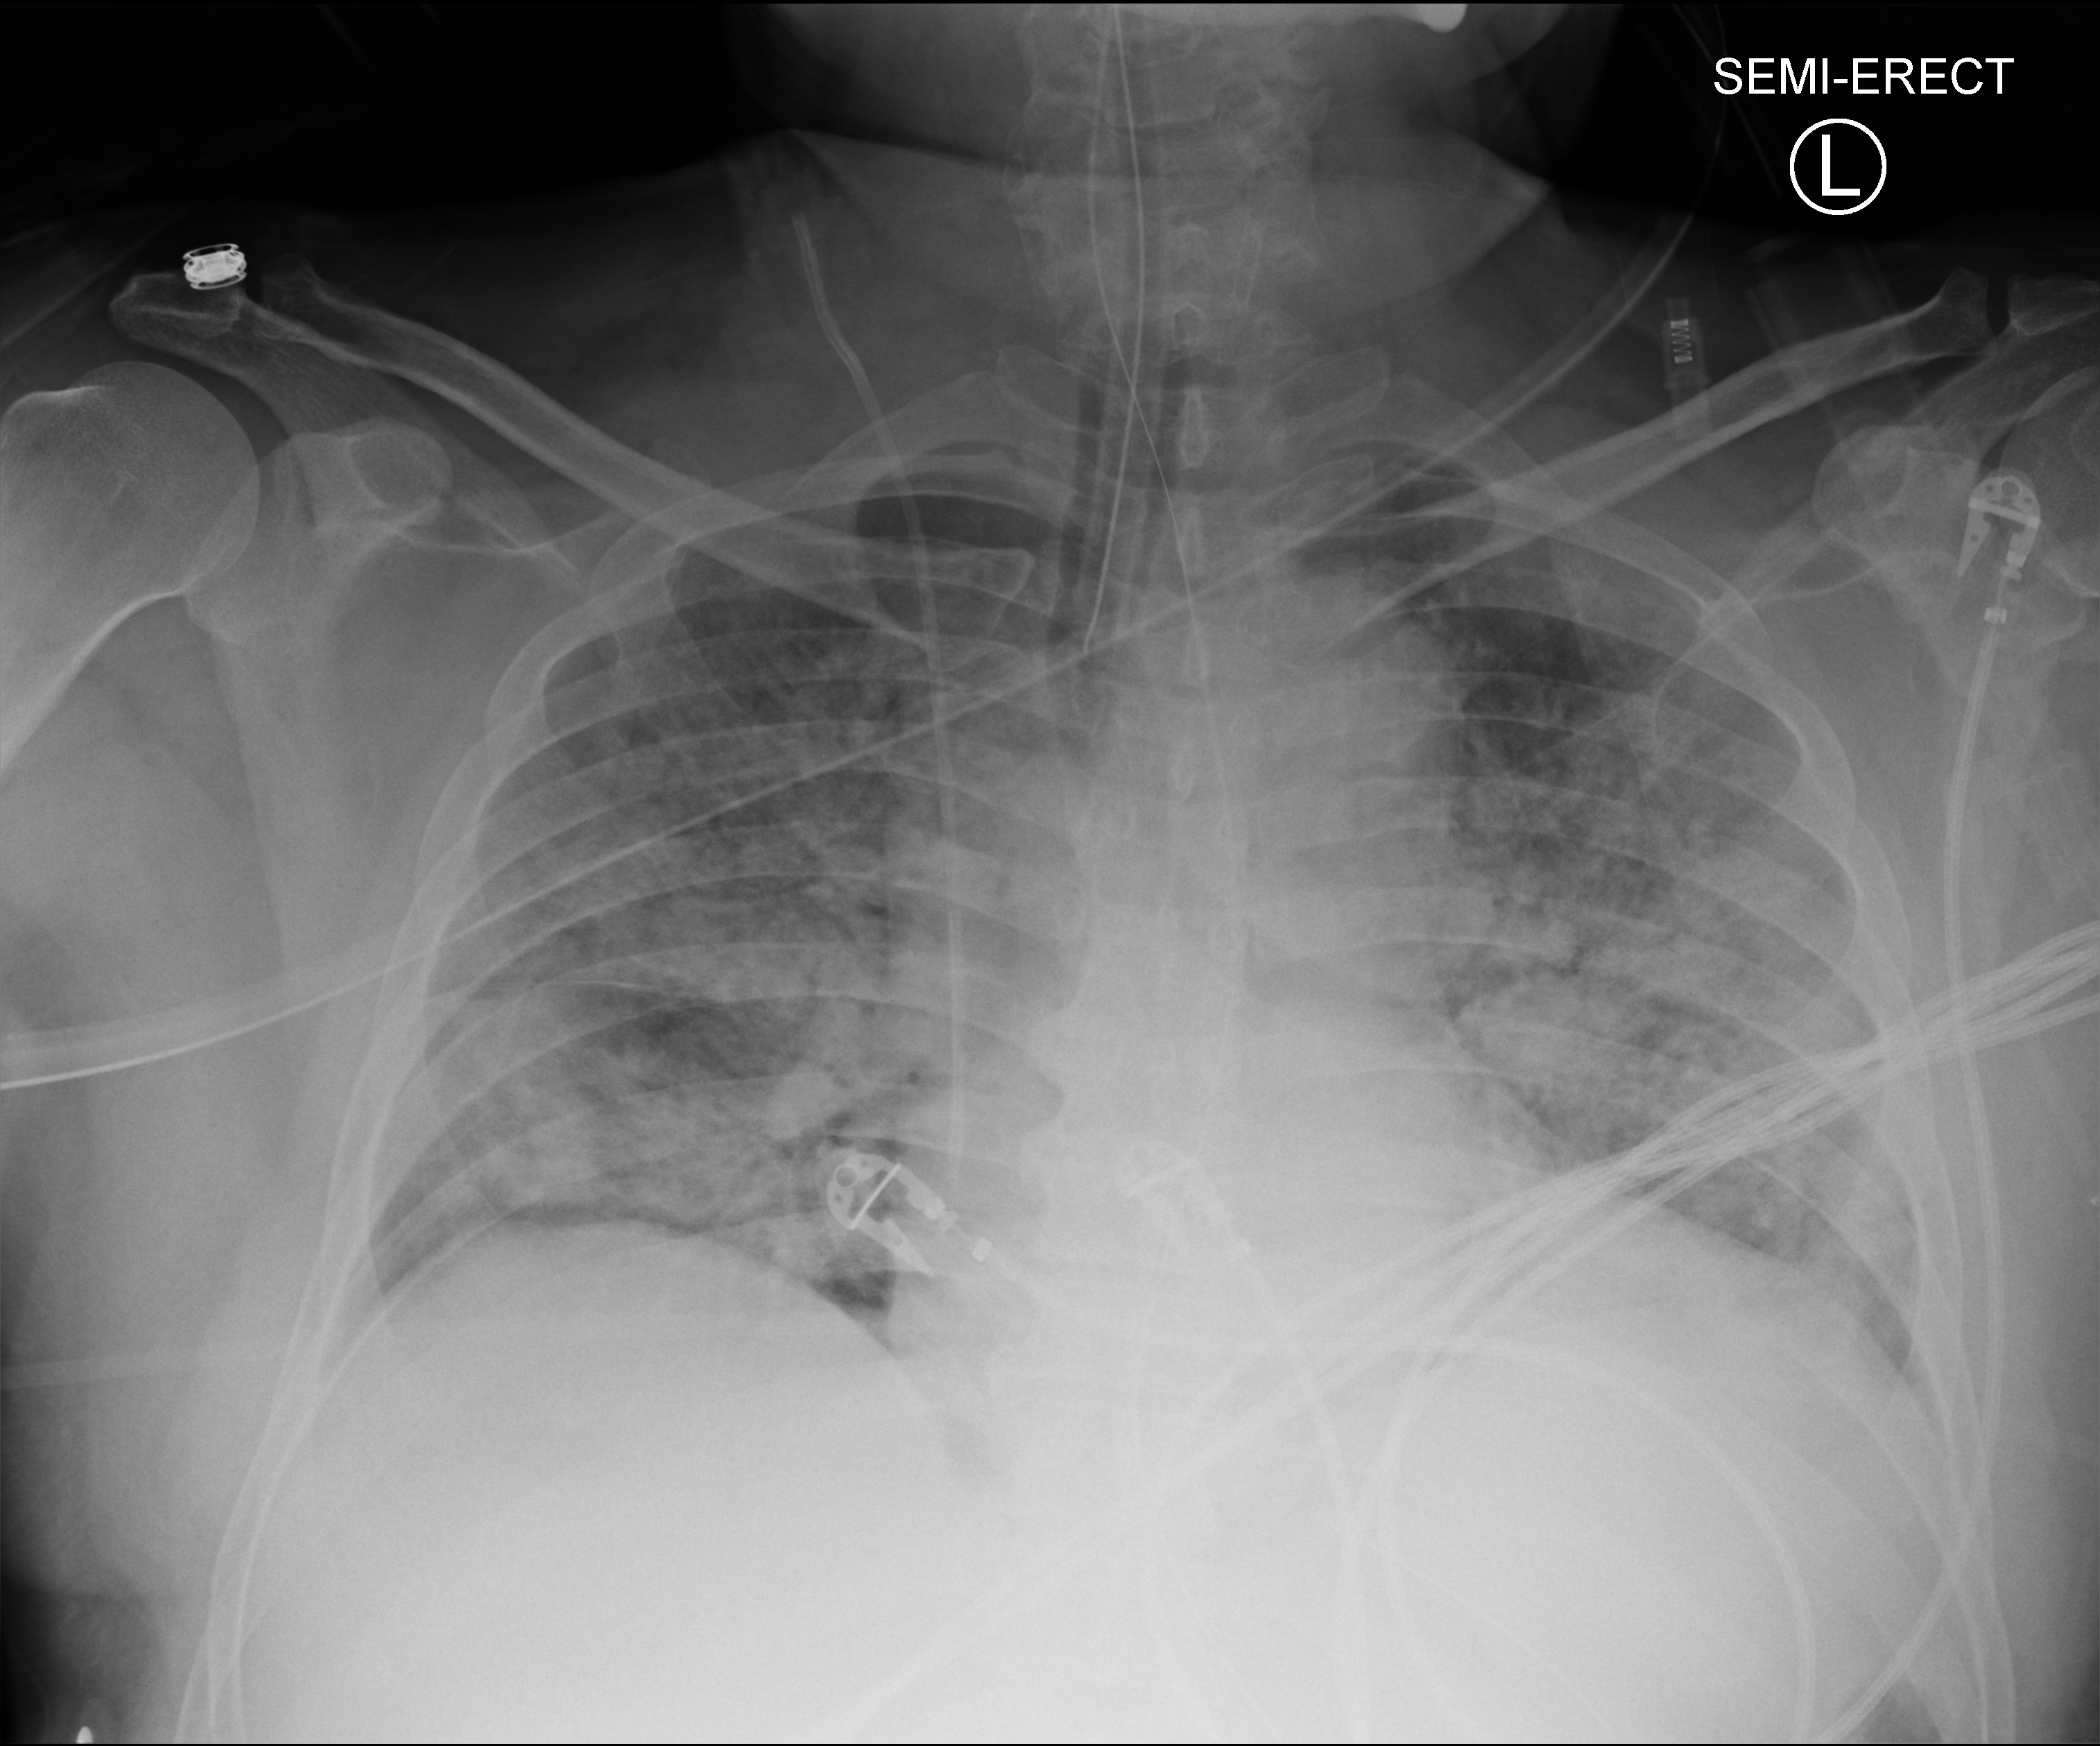
Chest X-ray (portable), anteroposterior (AP) projection. Male patient hospitalised with COVID-19, age 60–74 years.
From the hospital-stay record, not from the radiograph (when in the stay this image was taken is not recorded):
- COPD (admission record): no
- mechanically ventilated during this hospital stay: yes
- admitted to intensive care during this hospital stay: yes